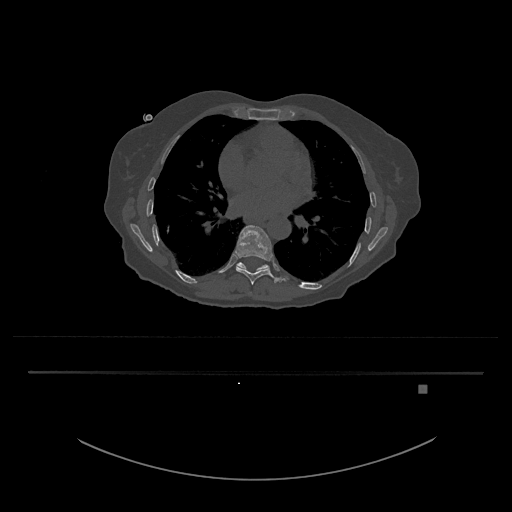
CT including the spine, one axial slice; position 750 of 797 along the scan axis; reconstruction kernel Br40s/3; bone window (W 1800 / L 400 HU); 0.5 mm slice thickness; 512 × 512 image matrix, field of view 500 × 500 mm. Patient: female, 57 years. Case-level facts recorded for this patient, not image findings: primary cancer: cervical.
Structures marked on this image (semi-automatically segmented with operator editing):
- T10 vertebra: bounding box [x1, y1, x2, y2] px = [236, 262, 270, 272]
- T8 vertebra: [250, 292, 252, 294]
- T9 vertebra: [235, 225, 284, 285]